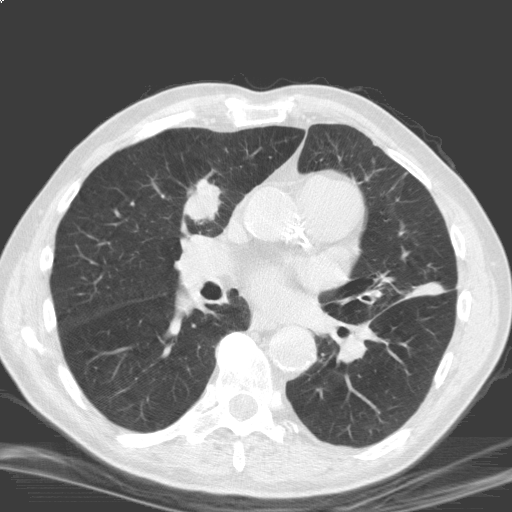
Axial slice from a low-dose chest CT screening exam, second annual screen, lung window (W 1500 / L -600 HU), 3.2 mm slice thickness, 120 kVp, slice 89 of 184 in the series, 512 × 512 image matrix, field of view 329 × 329 mm. Male participant, aged 69 years at enrolment. Current smoker at enrolment.
Lesion marked by an expert reader, bounding box [x1, y1, x2, y2] px = [171, 169, 231, 227]. The screening reader recorded 2 non-calcified nodules or masses ≥4 mm on this exam (right upper lobe, left lower lobe); which of them this box marks is not recorded. Later outcome: lung cancer diagnosed 17 days after this screen — squamous cell carcinoma, NOS, right upper lobe, moderately differentiated (G2), stage IB (AJCC 6th edition), 40 mm at pathology.